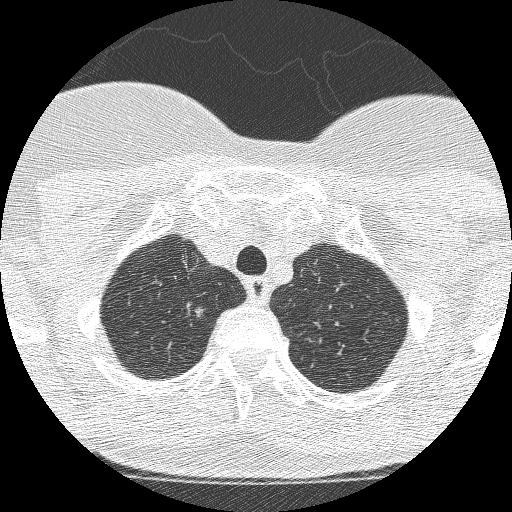
Axial slice from a low-dose chest CT screening exam. Second screening round (one year after baseline). Lung window (W 1500 / L -600 HU). 1.25 mm slice thickness. Lung (sharp) reconstruction kernel (BONE). Slice 211 of 250 in the series. 512 × 512 image matrix, field of view 257 × 257 mm. Female, age 61 years at enrolment.
Expert reader's lesion annotation, bounding box (x1, y1, x2, y2) in pixels: (172, 295, 216, 331). The exam's reader record, not a measurement of the box and not confirmed to be the same lesion: non-calcified nodule or mass ≥4 mm, right upper lobe, 11 × 8 mm, poorly defined margins, mixed attenuation, pre-existing on the prior screen: yes; interval growth: yes. Participant outcome: lung cancer diagnosed 28 days after this screen — adenocarcinoma, NOS, right upper lobe, poorly differentiated (G3), 12 mm at pathology.